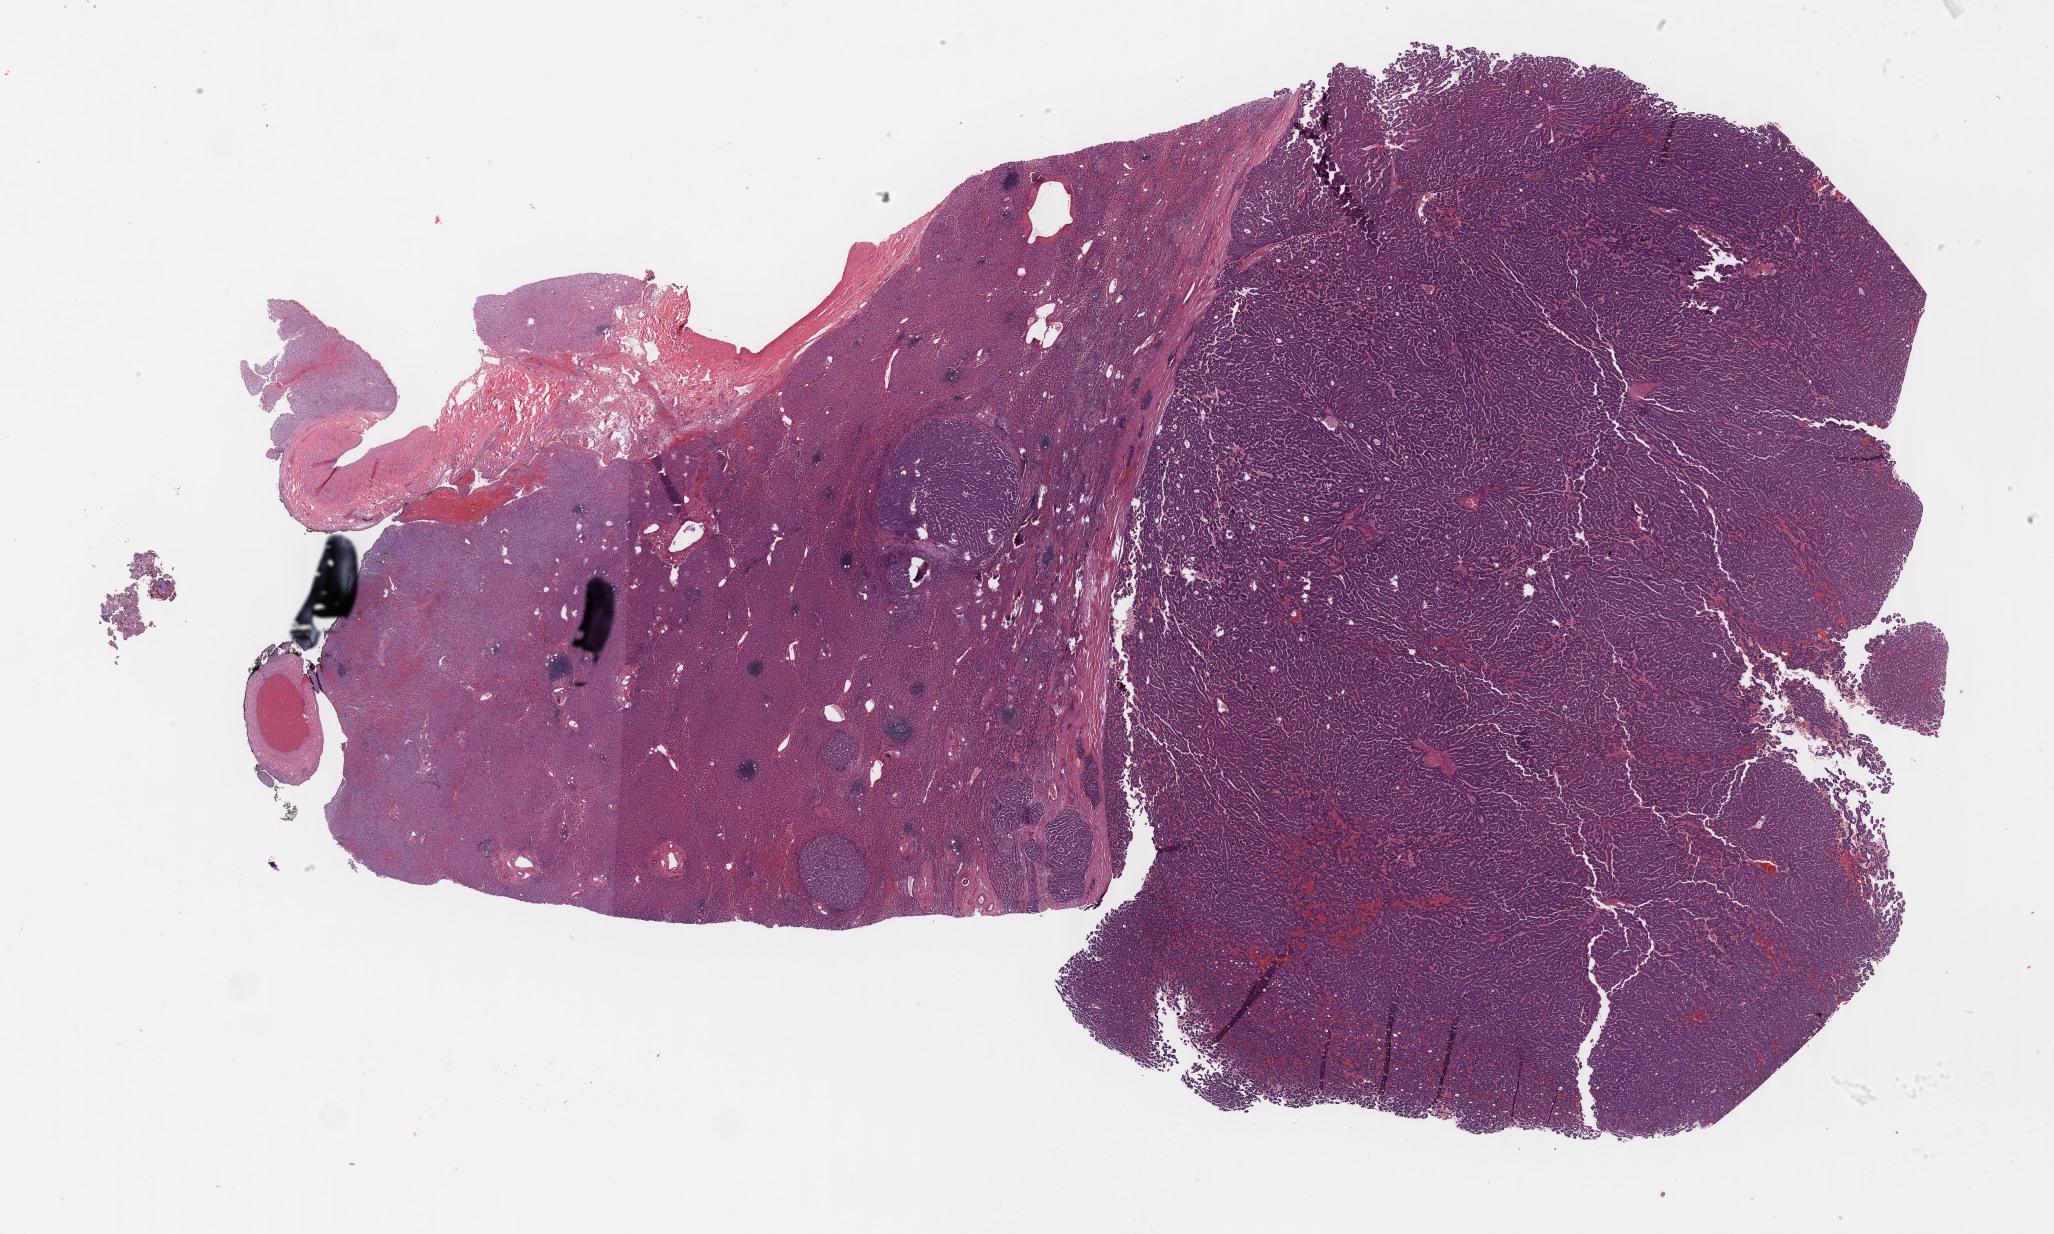
Whole-slide histology image, H&E — shown as a low-resolution overview of the whole scanned area (about 33.2 x 20.0 mm, slide scanned at 40x). FFPE section. Liver, primary tumour sample. Male patient; age at initial diagnosis 61 years. Histologic grade: G1 (well differentiated).
Histologic diagnosis: Hepatocellular carcinoma, NOS.